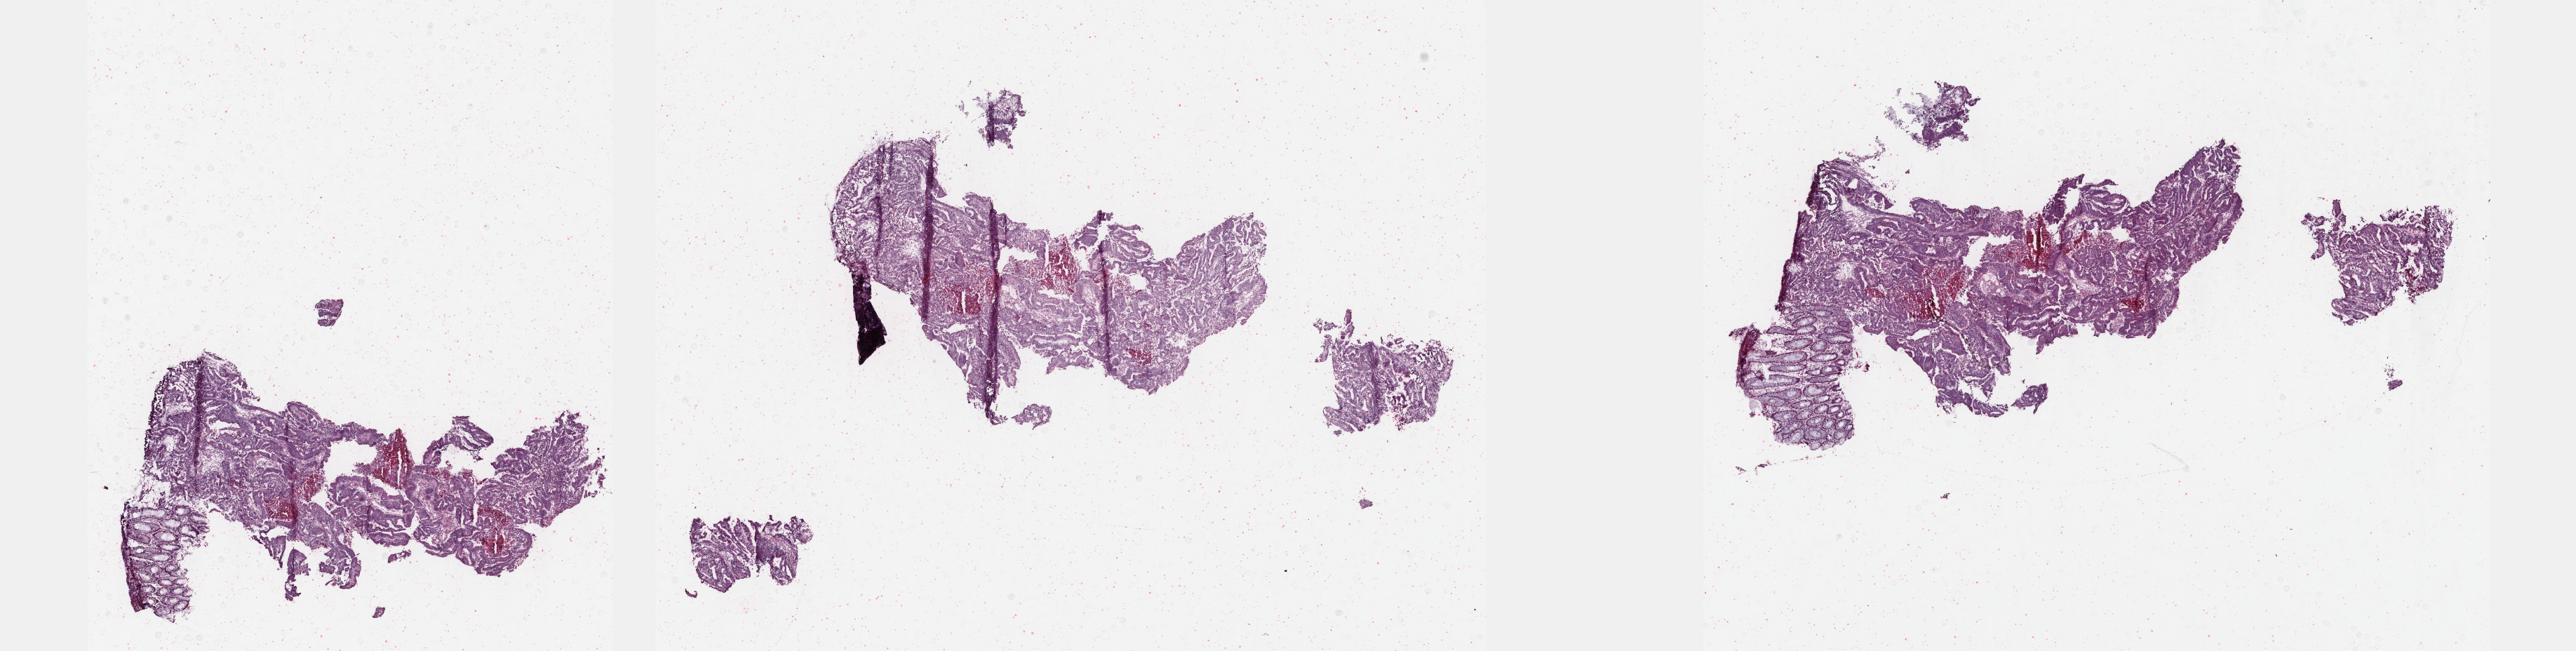
Whole-slide histology image, H&E-stained, whole scanned area (about 29.7 x 7.5 mm, slide scanned at 40x) shown as a low-resolution overview; frozen section; sample: primary tumour, colon. Female, age 70 years at initial diagnosis. Slide review estimates, as recorded: tumour cells 75%, tumour nuclei 80%, normal cells 10%, stromal cells 5%, necrosis 10%. Inflammatory infiltration, as recorded: lymphocyte infiltration 8%, monocyte infiltration 1%, neutrophil infiltration 2%.
AJCC pathologic stage: IV (6th edition). TNM: T3 N0 M1. Pathologic diagnosis: Adenocarcinoma, NOS (sigmoid colon). Lymph nodes positive (case pathology): 0 of 13 examined.